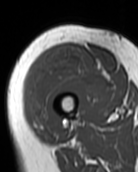
MRI of an extremity soft-tissue mass, one axial slice. Position 31 of 99 along the scan axis. MR volume resampled by the dataset authors to the PET/CT grid (not the native acquisition matrix). 3.27 mm slice thickness. 138 × 172 image matrix, field of view 135 × 168 mm. Female patient. Case-level facts recorded for this patient, not image findings: histological type: pleiomorphic undifferentiated sarcoma; grade: high; site of the primary tumour: right quadricep.
Structures marked on this image (expert contour drawn on MRI and transferred to this co-registered scan by the dataset authors):
- gross tumour volume including surrounding oedema: bounding box [x1, y1, x2, y2] px = [26, 50, 109, 129]
- gross tumour volume (mass): [26, 50, 109, 129]